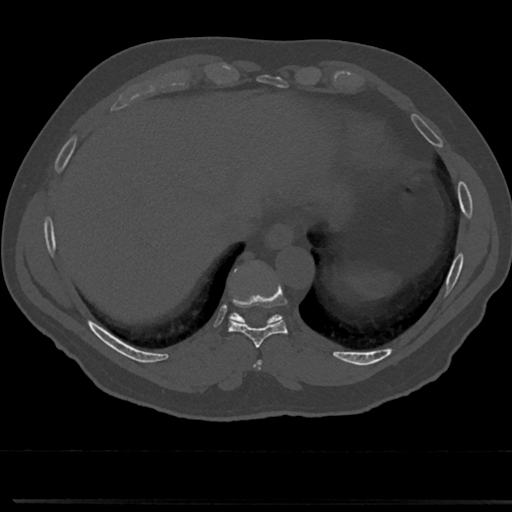
CT including the spine, one axial slice; position 293 of 817 along the scan axis; bone window (W 1800 / L 400 HU); 0.5 mm slice thickness; 512 × 512 image matrix, field of view 355 × 355 mm. Patient: male, 61 years. Case-level facts recorded for this patient, not image findings: primary cancer: prostate.
Annotated regions visible in this slice (semi-automatically segmented with operator editing):
- T8 vertebra: bounding box (x1, y1, x2, y2) in pixels: (252, 337, 267, 362)
- T9 vertebra: (216, 266, 298, 349)